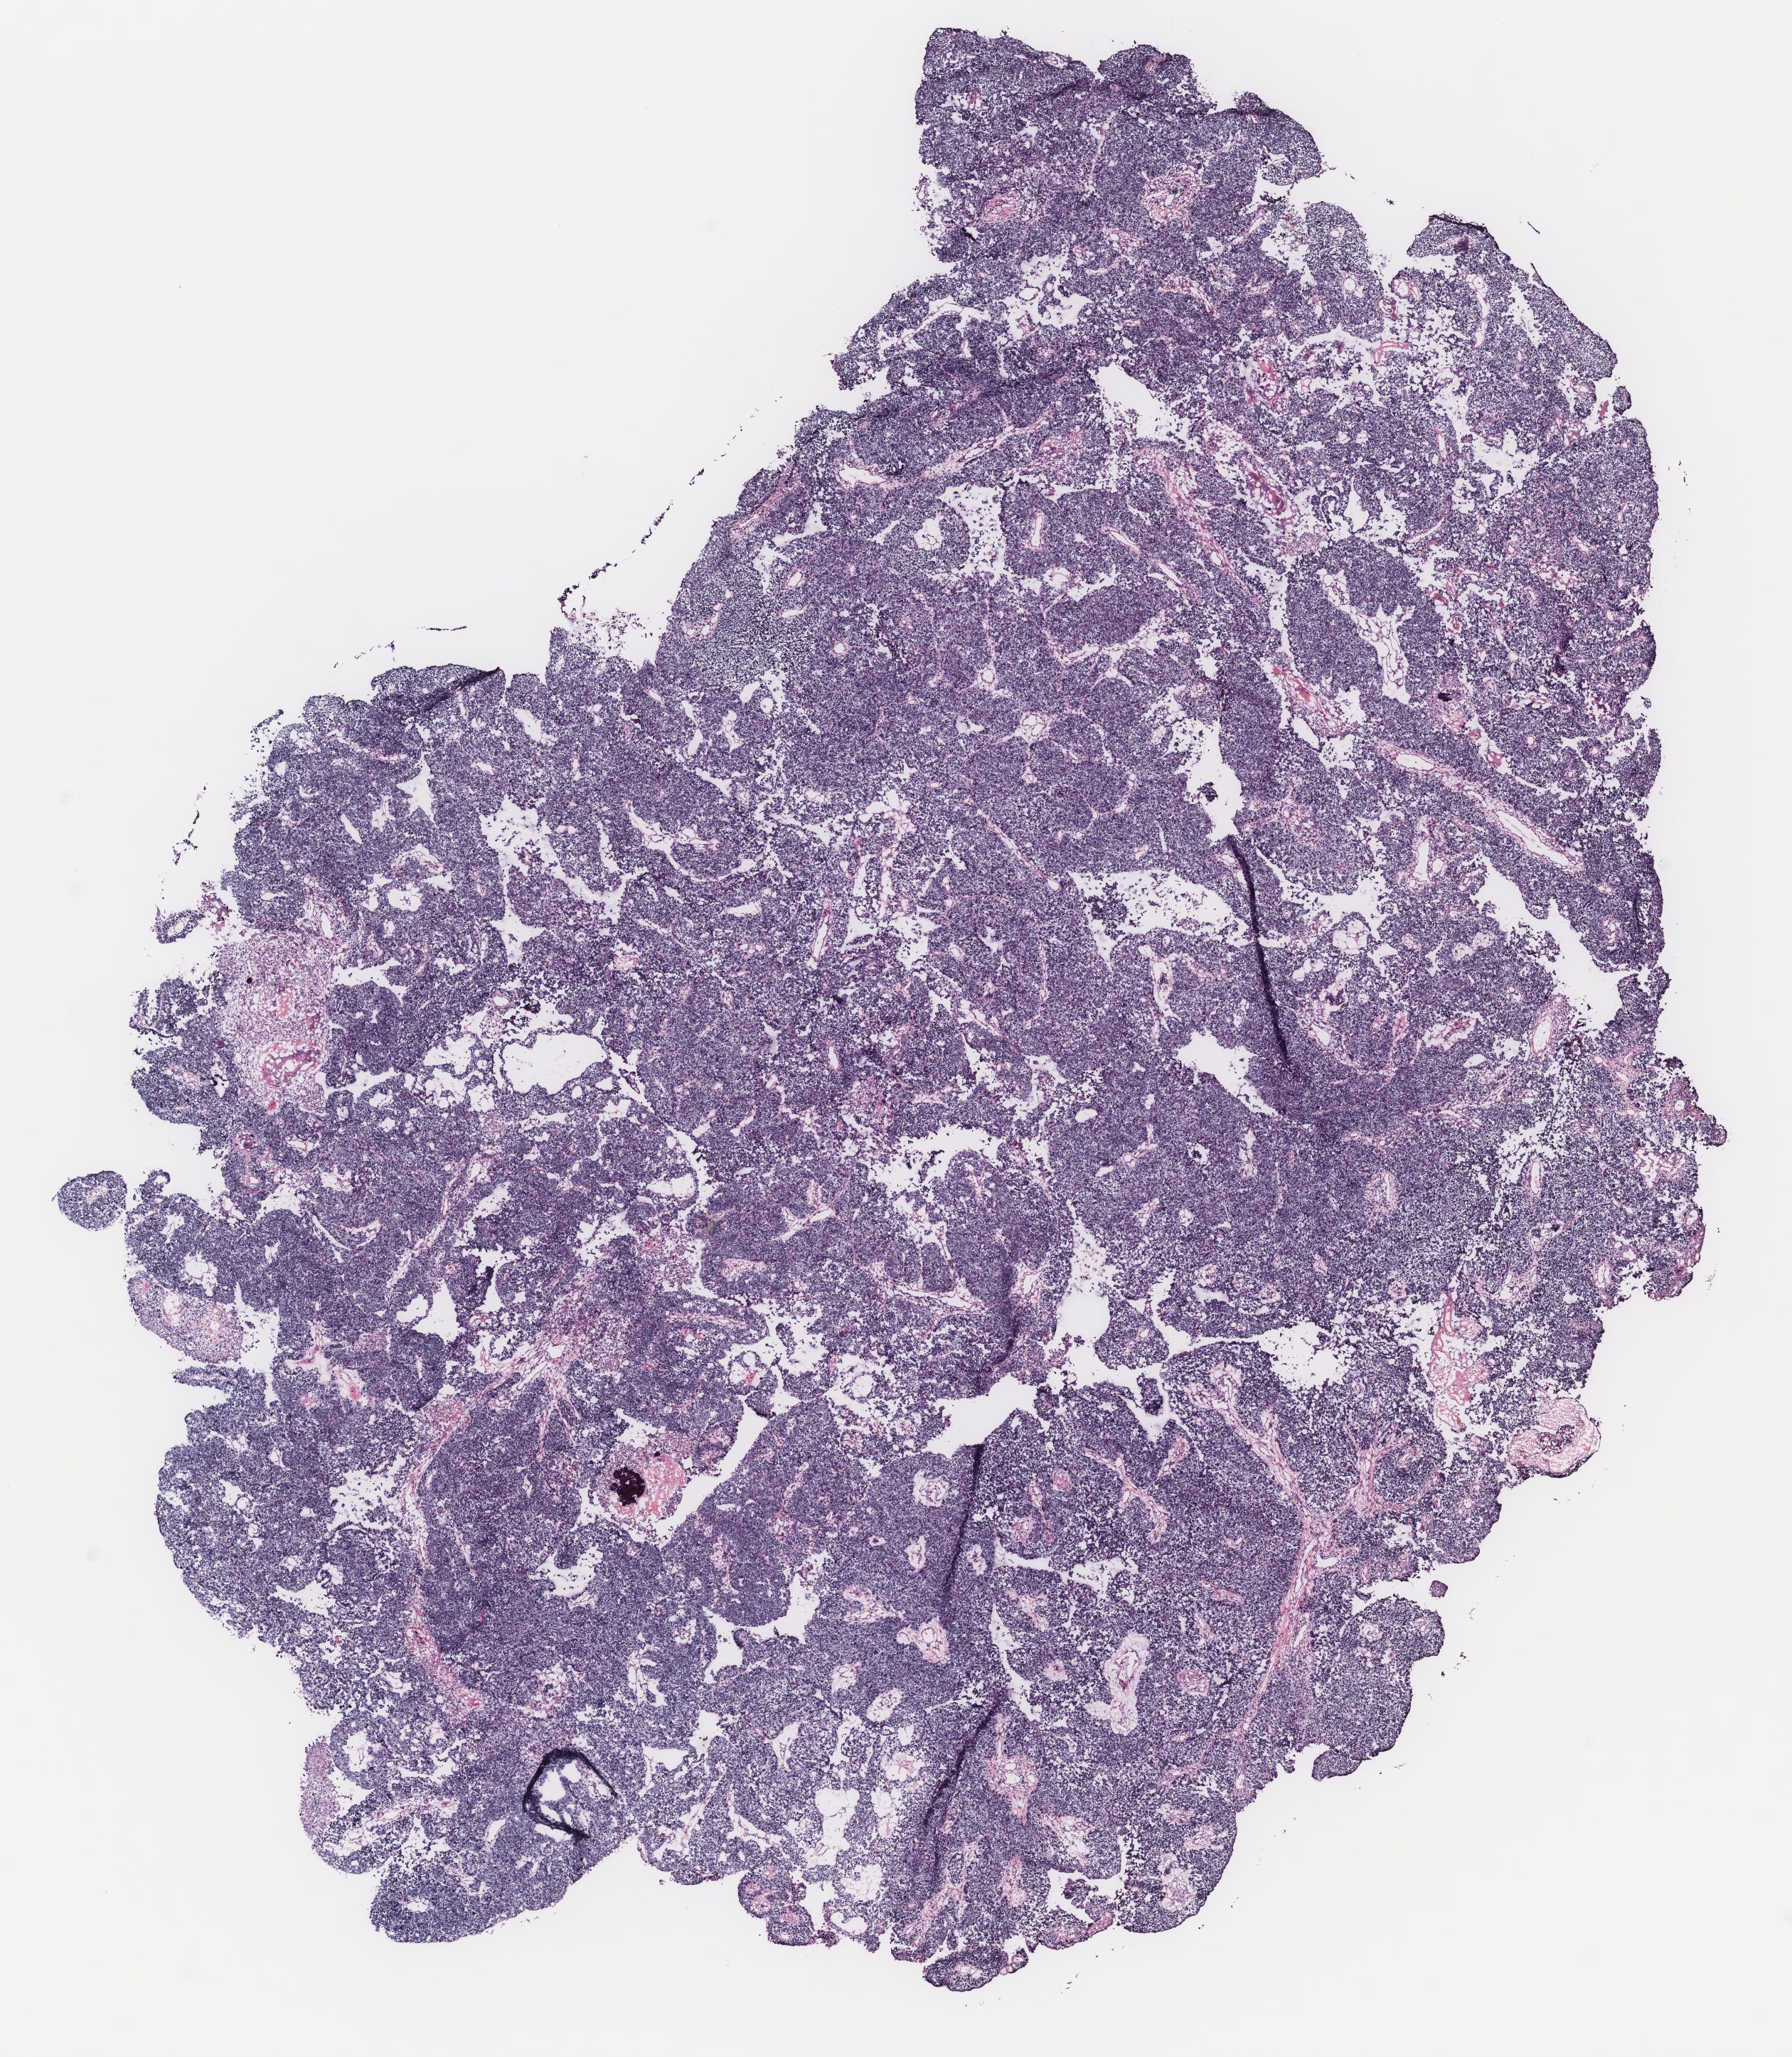
Whole-slide histology image, Hematoxylin and eosin (H&E) stained, low-resolution overview of the scanned area, about 10.1 x 11.6 mm (acquisition: 40x scan). Ovary, tissue type not recorded.
* patient diagnosis (cohort enrolment): ovarian cancer (ovary)